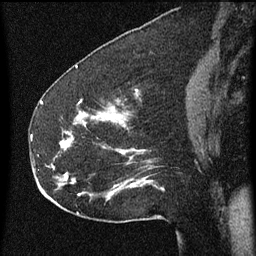
Breast MRI (dynamic contrast-enhanced), one sagittal slice; position 26 of 60 along the scan axis; dynamic contrast-enhanced series, image 2 of 3 at this slice position (ordered by acquisition); 1.5 T; TE 4.2 ms, TR 8 ms; 2 mm slice thickness; 256 × 256 image matrix, field of view 180 × 180 mm. Patient: female, 52 years.
Outlined on this slice (semi-automatic segmentation, software-assisted and operator-edited):
- analysis volume of interest (the breast-tissue region the enhancement analysis was run in; not a lesion): bounding box (x1, y1, x2, y2) in pixels: (54, 110, 165, 207)
- tumour enhancement mask (voxels above the 70 % enhancement threshold inside the analysis volume of interest): (60, 114, 164, 191)